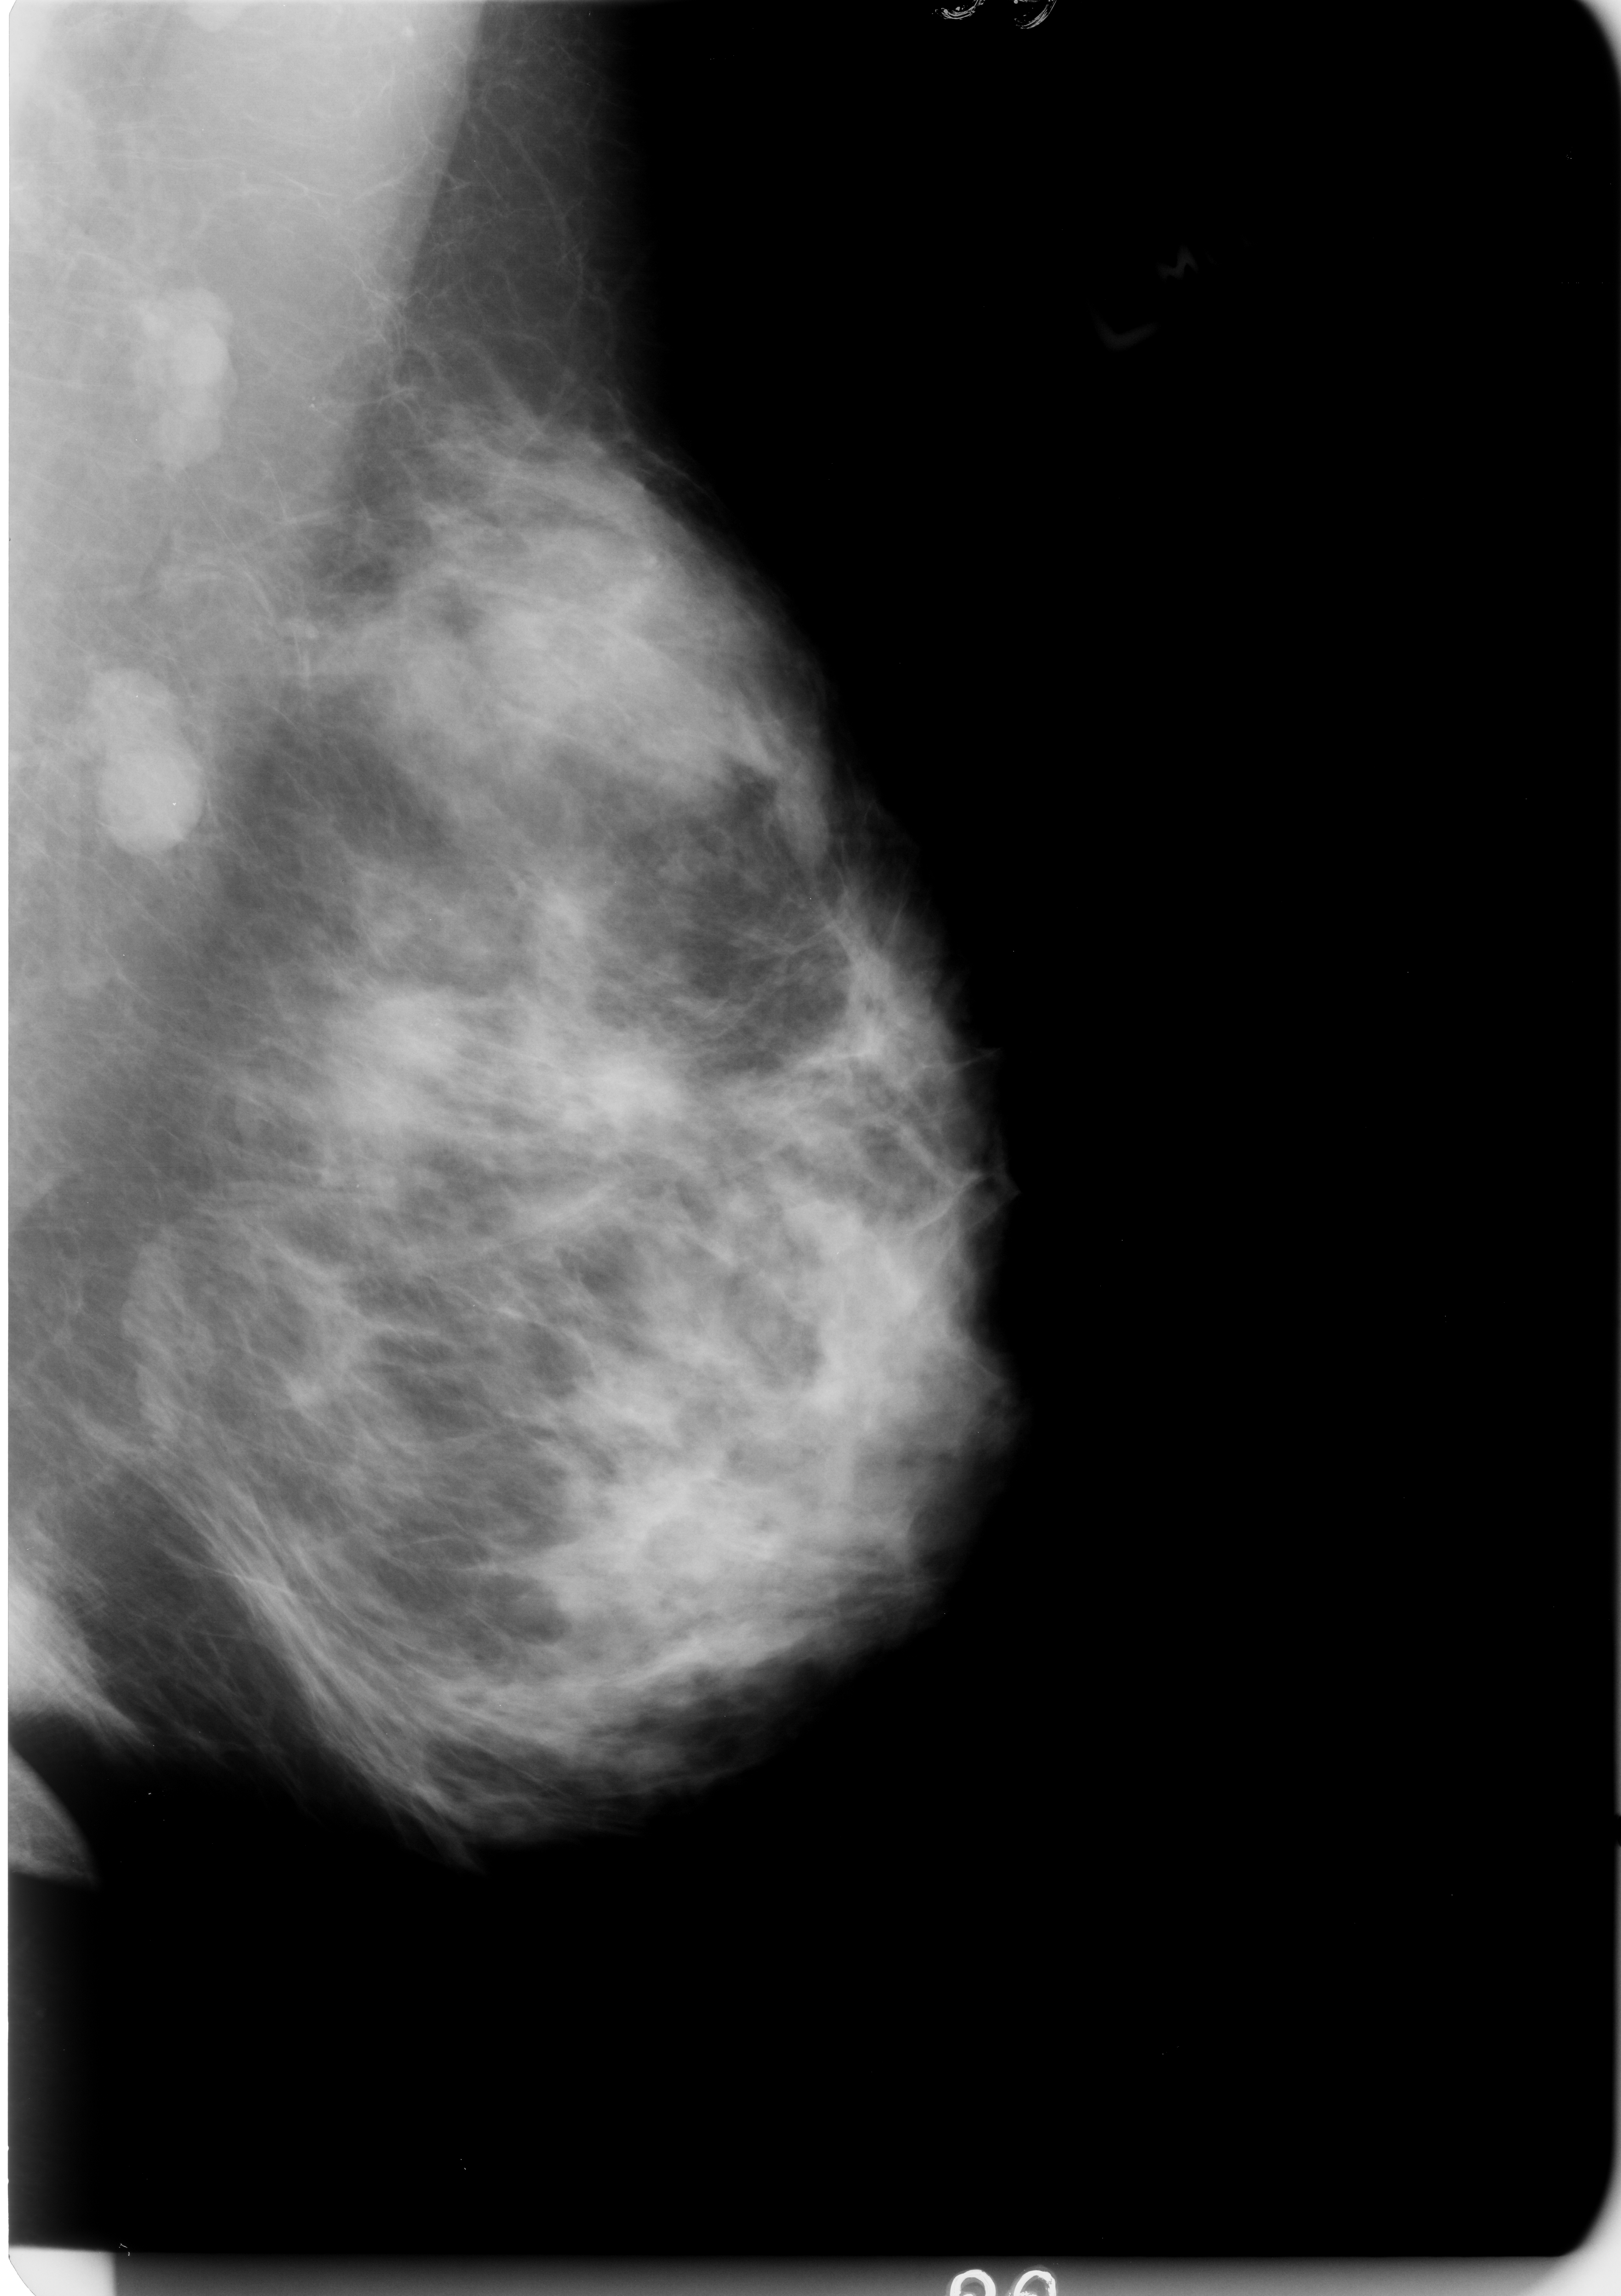
Scanned film-screen mammogram; left breast; mediolateral oblique (MLO) view; breast composition: heterogeneously dense (BI-RADS density category 3 of 4).
Radiologist-marked abnormalities on this image: calcifications, morphology pleomorphic, distribution clustered; BI-RADS assessment category 4; subtlety rating 3 on a 1 (subtle) to 5 (obvious) scale; pathology result (as recorded, not read from the image): malignant.